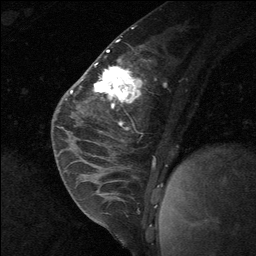
Breast MRI (dynamic contrast-enhanced), one sagittal slice. Position 29 of 64 along the scan axis. Dynamic contrast-enhanced study with each time point stored as its own series, time point 2 of 3 at this slice position (early post-contrast, ordered by acquisition time). 1.5 T. TE 4.8 ms, TR 27 ms. 256 × 256 image matrix, field of view 180 × 180 mm. Female patient, age 26 years. From the clinical record (not read from this slice): setting: breast cancer imaged before/during neoadjuvant chemotherapy; receptor status: HR-positive, HER2-negative.
Outlined on this slice (semi-automatically segmented with operator editing):
- analysis volume of interest (the breast-tissue region the enhancement analysis was run in; not a lesion): bounding box [x1, y1, x2, y2] px = [86, 43, 129, 137]
- tumour enhancement mask (voxels above the 90 % enhancement threshold inside the analysis volume of interest): [94, 70, 116, 92]